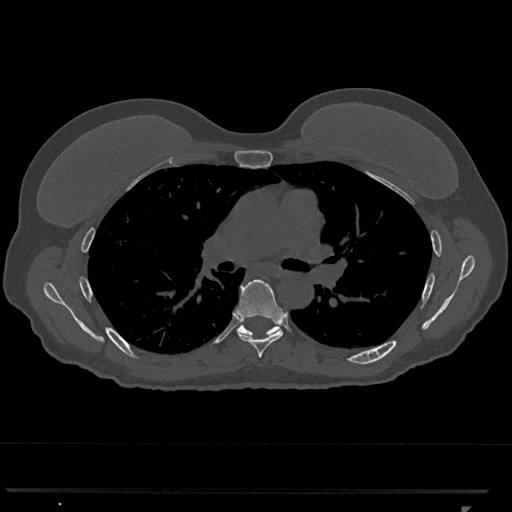
CT including the spine, one axial slice; 120 kVp; bone window (W 1800 / L 400 HU); 0.5 mm slice thickness; 512 × 512 image matrix, field of view 380 × 380 mm. Female patient, age 62 years. From the clinical record (not read from this slice): primary cancer: renal.
Outlined on this slice (semi-automatic segmentation, software-assisted and operator-edited):
- T6 vertebra: bounding box <237,279,285,358> (left, top, right, bottom; pixels)
- T7 vertebra: <237,324,279,337>